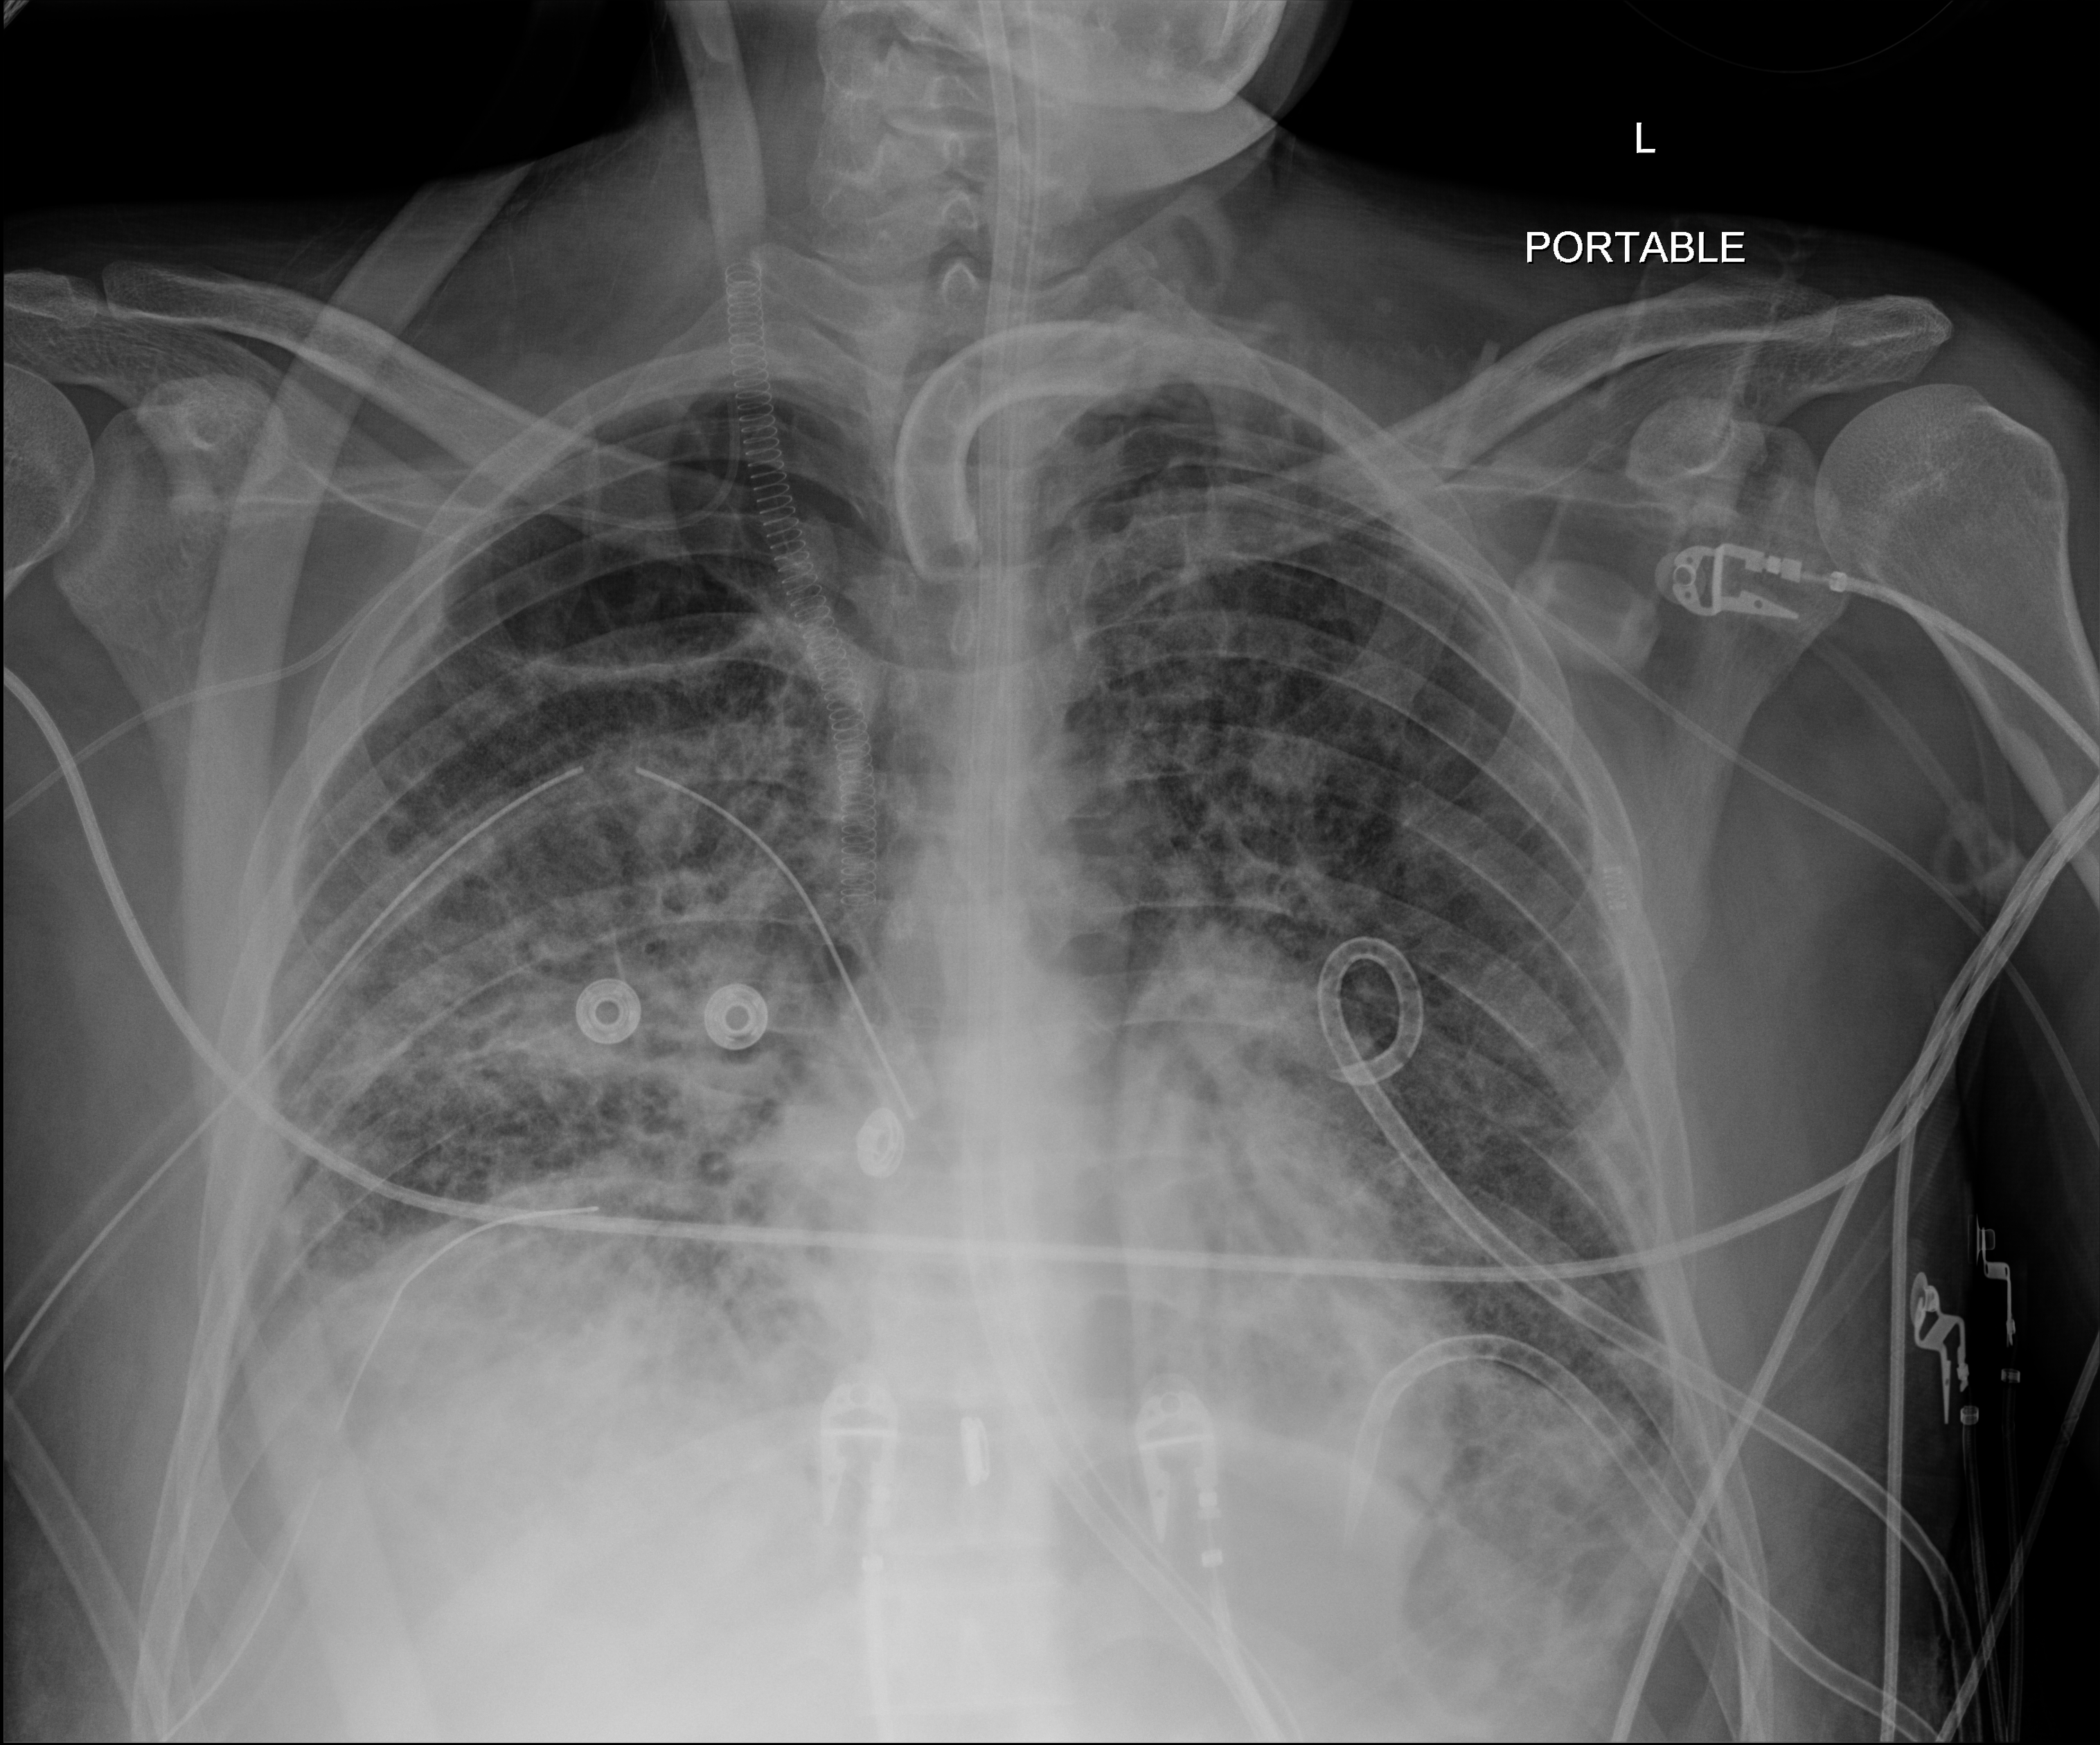
Portable chest radiograph, anteroposterior (AP) projection. Patient hospitalised with COVID-19, aged 18–59 years.
From the hospital-stay record, not from the radiograph (when in the stay this image was taken is not recorded): other chronic lung disease (admission record): no.